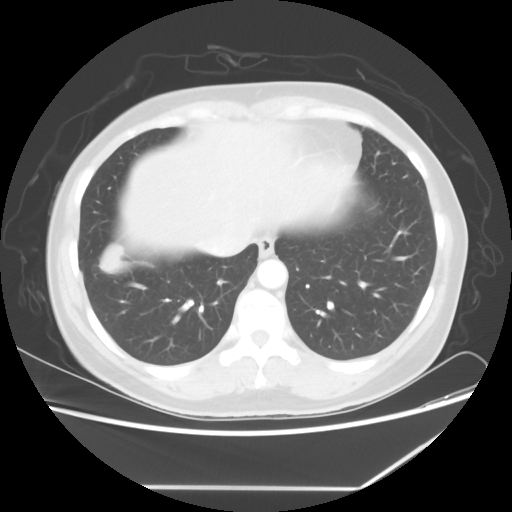
Chest CT, one axial slice. Position 18 of 60 along the scan axis. 100 kVp. Lung window (W 1500 / L -600 HU). 5 mm slice thickness. 512 × 512 image matrix, field of view 374 × 374 mm. Patient: female, 42 years. From the clinical record (not read from this slice): clinical TNM (as recorded): T2 N1 M0.
Annotated regions visible in this slice (bounding box drawn by a radiologist):
- lung tumour (recorded histology: adenocarcinoma): box from (x=95, y=239) to (x=130, y=277) px